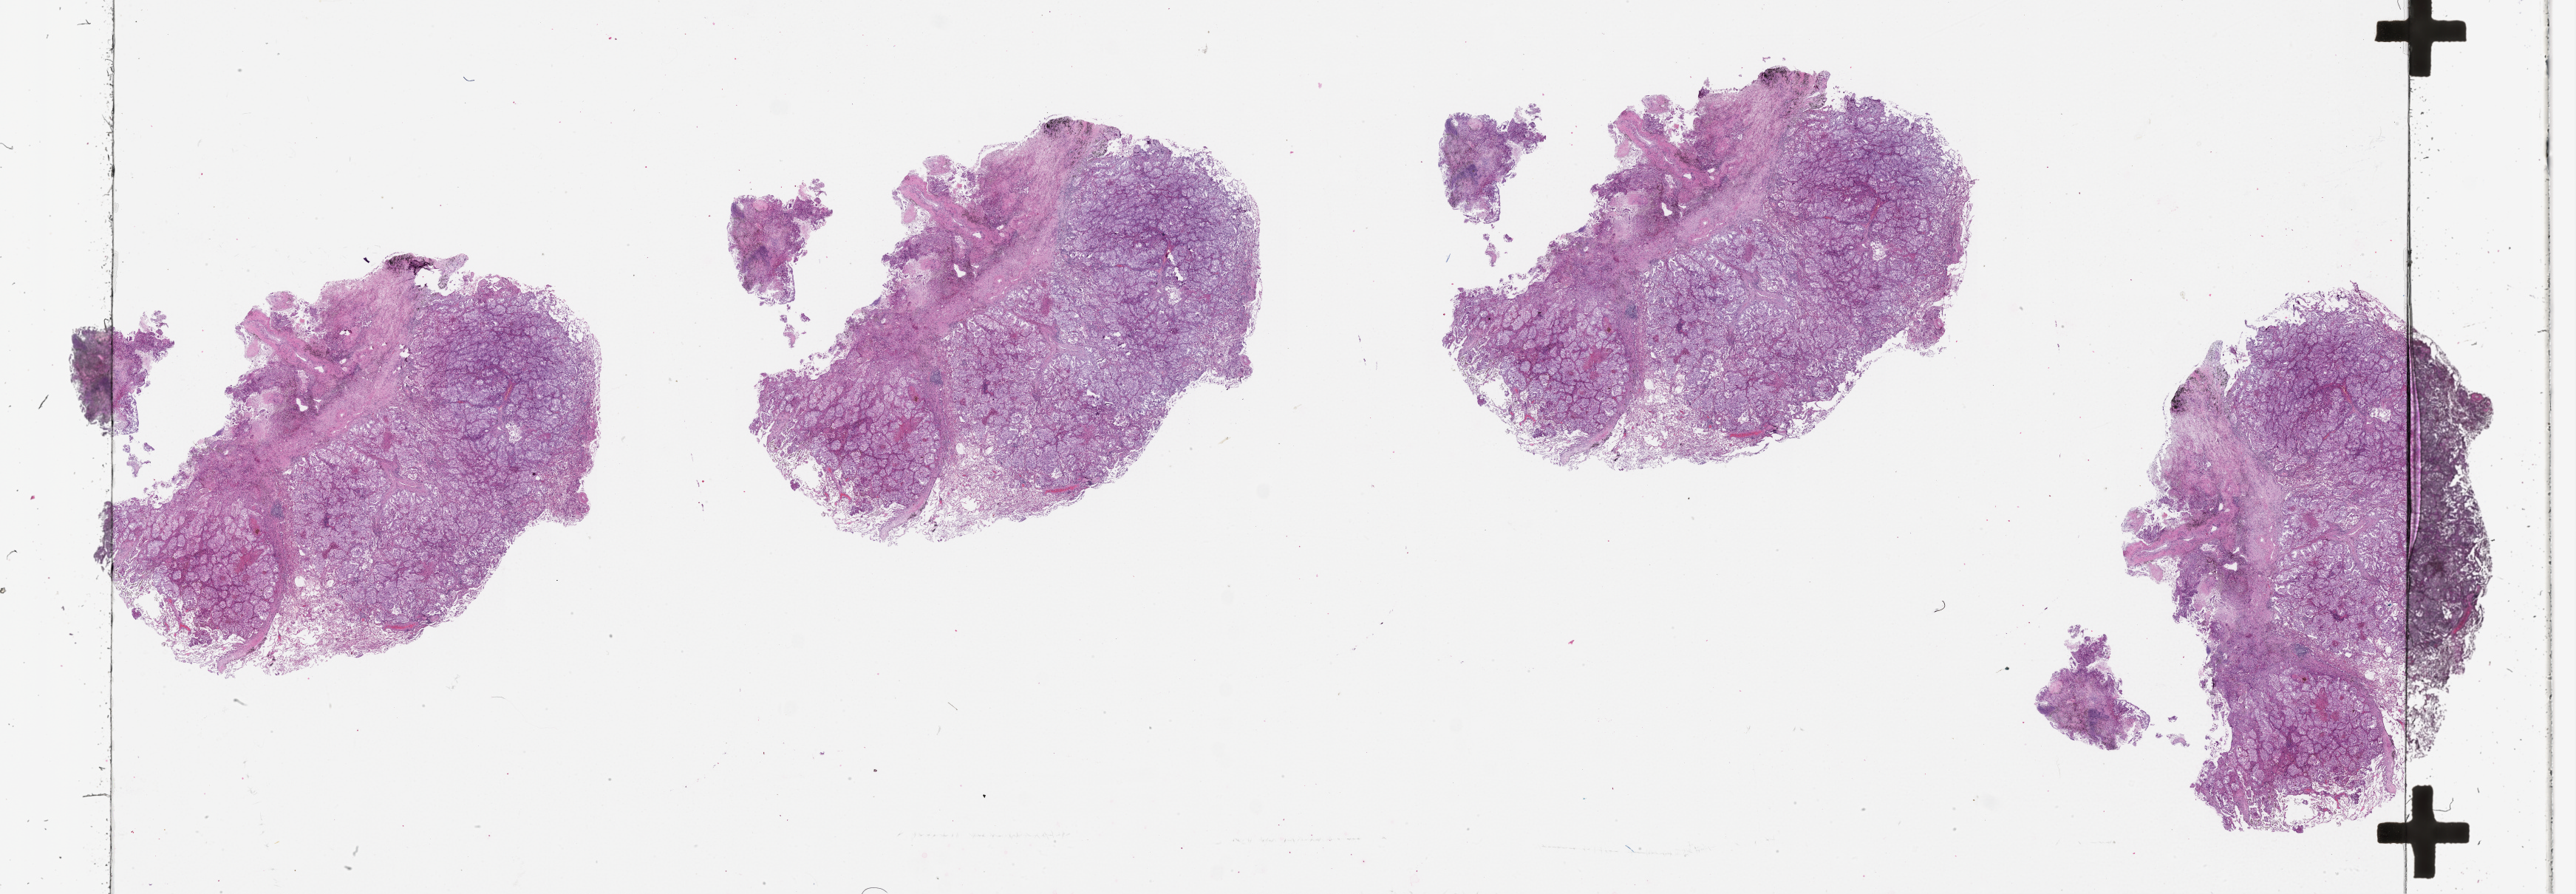
Whole-slide histology image, H&E — low-resolution overview of the scanned area, about 56.1 x 19.5 mm (slide scanned at 20x); lung, tissue type not recorded.
Patient diagnosis (cohort enrolment): lung adenocarcinoma (lung).